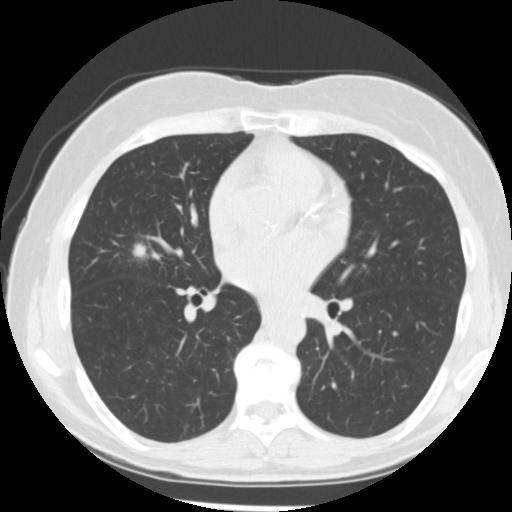
Chest CT (low-dose screening protocol), one axial image, first (baseline) screen, lung window (W 1500 / L -600 HU), 2.5 mm slice thickness, standard (soft-tissue) reconstruction kernel (STANDARD), slice 118 of 255 in the series, 512 × 512 image matrix, field of view 320 × 320 mm. Female, age 66 years at enrolment. Former smoker at enrolment.
Expert-annotated lung lesion, bounding box <125,239,161,270> (left, top, right, bottom; pixels). The exam's reader record, not a measurement of the box and not confirmed to be the same lesion: non-calcified nodule or mass ≥4 mm, right middle lobe, 15 × 13 mm, poorly defined margins, soft tissue attenuation. Official screen result: positive, change unspecified: nodule(s) >= 4 mm or enlarging nodule(s), mass(es), or other non-specific abnormalities suspicious for lung cancer. Lung cancer was diagnosed 27 days after this screen: adenocarcinoma, NOS, right middle lobe, undifferentiated (G4), stage IIIA (AJCC 6th edition), 18 mm at pathology.